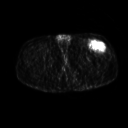
FDG PET of an extremity soft-tissue mass (from a PET/CT study), one axial slice; position 252 of 267 along the scan axis; 3.27 mm slice thickness; 128 × 128 image matrix. Male patient, age 64 years. From the clinical record (not read from this slice): histological type: extraskeletal osteosarcoma; grade: high; site of the primary tumour: thigh.
Outlined on this slice (expert contour drawn on MRI and transferred to this co-registered scan by the dataset authors):
- gross tumour volume (mass): bounding box [x1, y1, x2, y2] px = [90, 42, 105, 51]